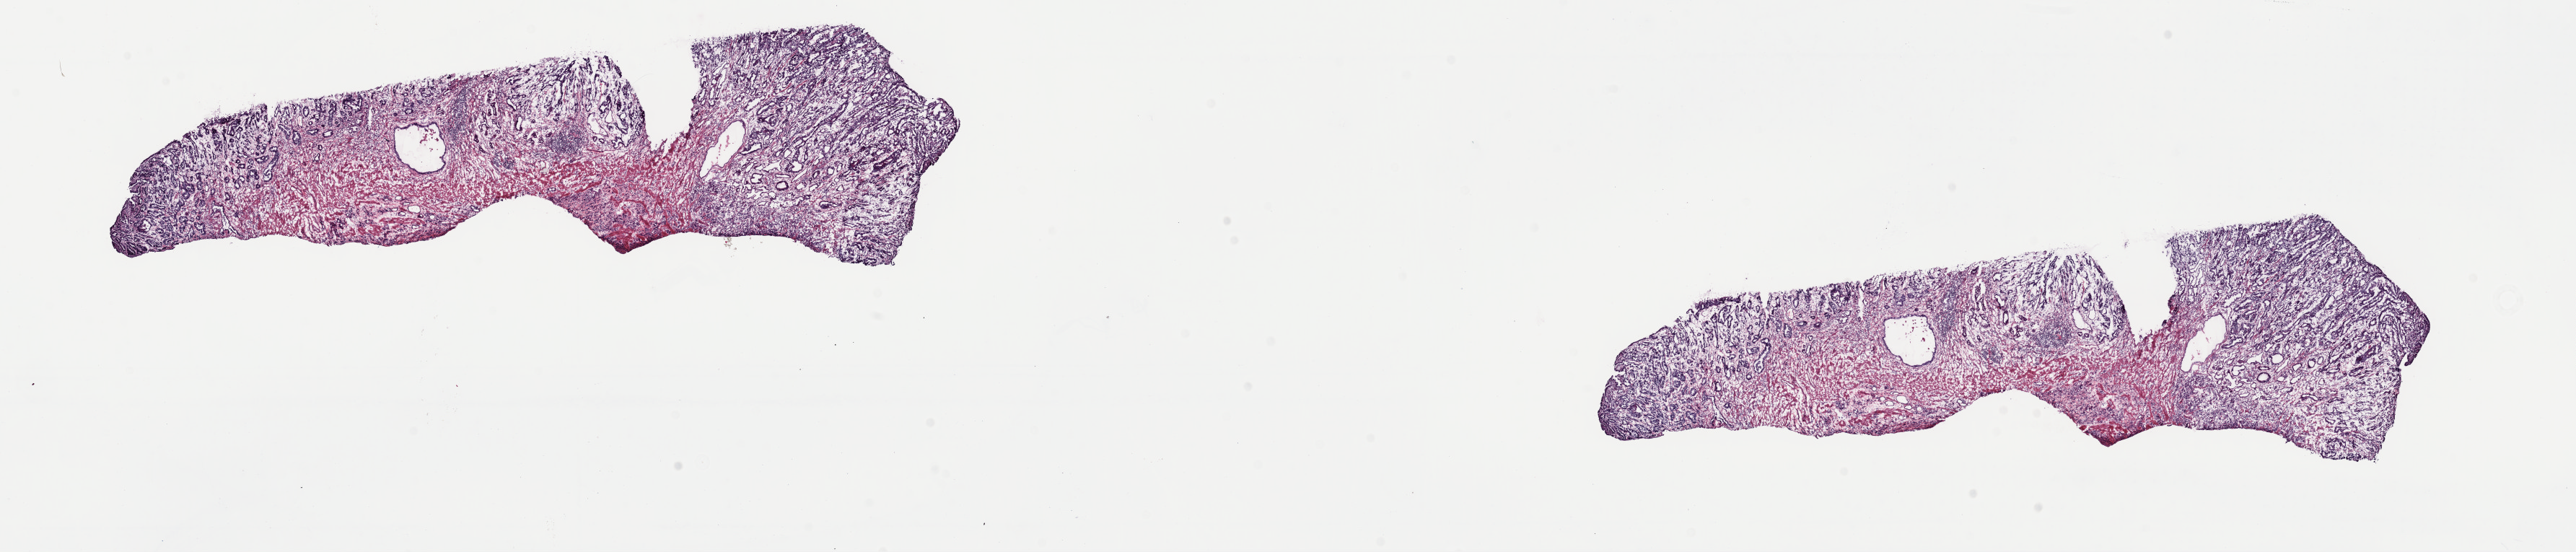
Digitized H&E tissue section (whole slide) — a low-resolution overview of the entire scanned area, about 28.2 x 6.0 mm. Frozen section. Stomach, primary tumour sample. Female, age 62 years at initial diagnosis. Histologic grade: G2 (moderately differentiated). Slide review estimates, as recorded: tumour cells 15%, tumour nuclei 20%, normal cells 50%, stromal cells 35%, necrosis 0%. Infiltration values recorded for this section: lymphocyte infiltration 100%, monocyte infiltration 0%, neutrophil infiltration 0%.
* AJCC pathologic stage: IIA (7th edition)
* lymph nodes positive (case pathology): 2 of 63 examined
* histologic diagnosis: Carcinoma, diffuse type